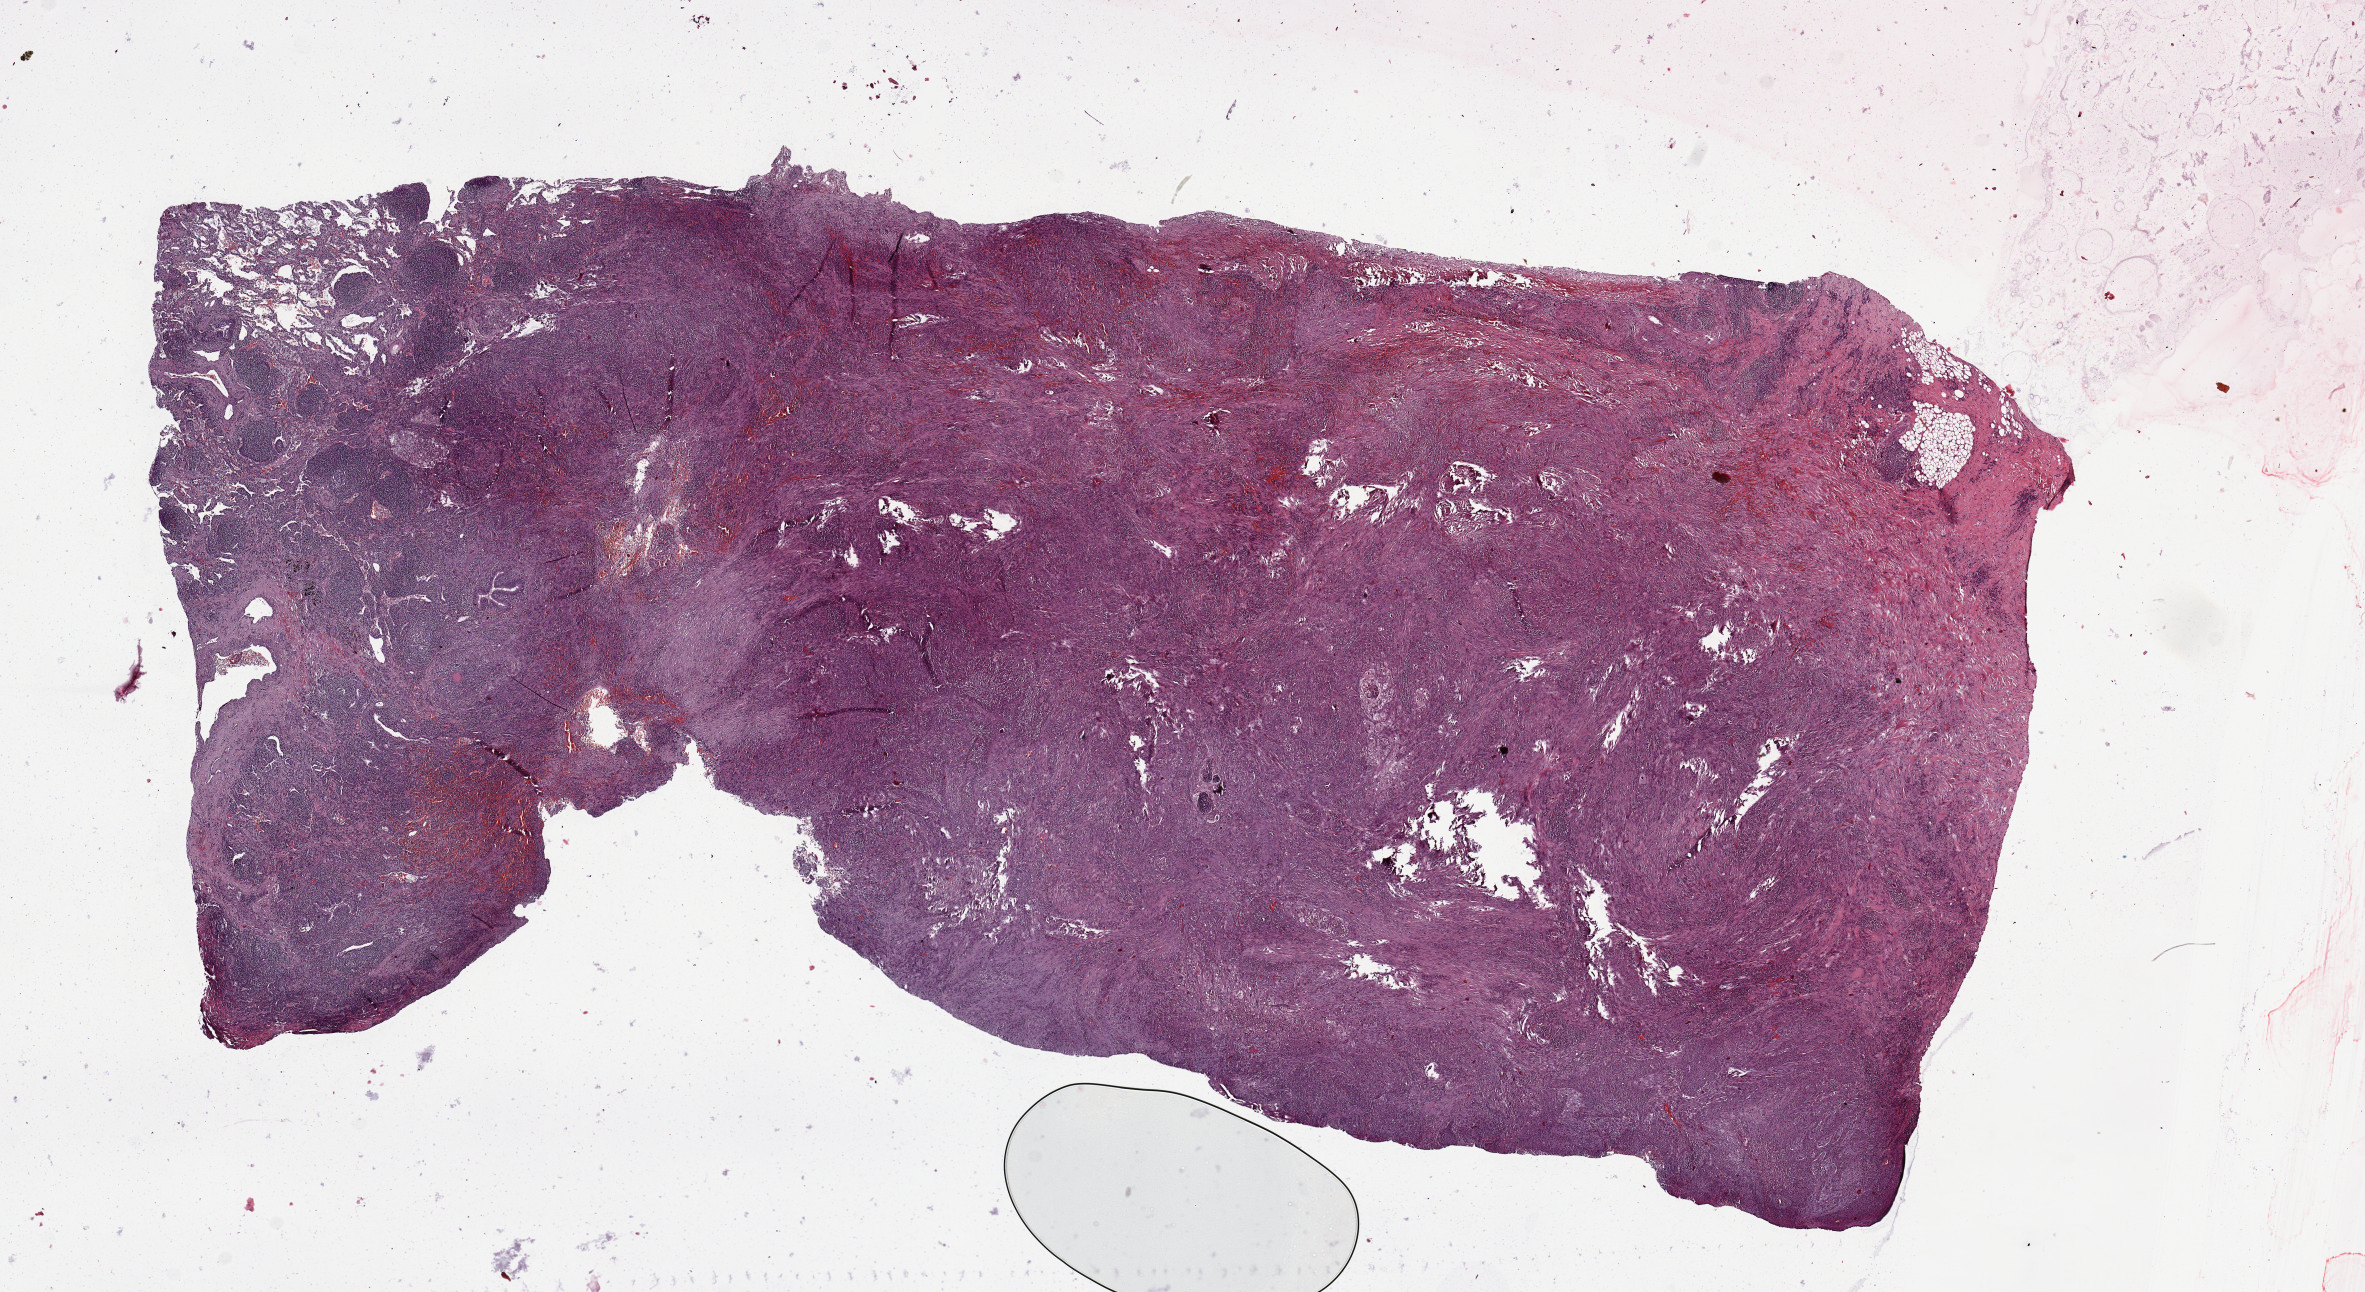
H&E whole-slide image — whole scanned area (about 18.7 x 10.2 mm) shown as a low-resolution overview; tumour tissue sample, sampled site: lung. 58-year-old male patient. Histologic grade: G2 (moderately differentiated). Composition of this section per pathologist review: tumour nuclei 65%, necrosis 5%.
Primary tumour site (as recorded): left upper lobe. AJCC pathologic stage: IIB. Diagnosis: Squamous cell carcinoma, NOS.